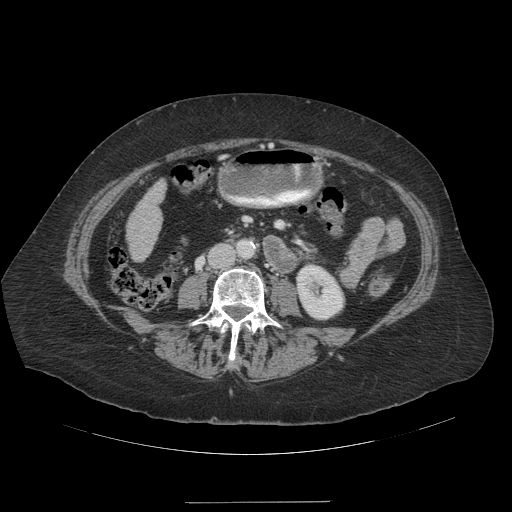
Contrast-enhanced abdominal CT (liver protocol), one axial slice. Slice 30 of 99 in the series (ordered by position). 140 kVp. Soft-tissue window (W 400 / L 40 HU). 2.5 mm slice thickness. 512 × 512 image matrix, field of view 440 × 440 mm. From the clinical record (not read from this slice): diagnosis: hepatocellular carcinoma (patient treated with transarterial chemoembolisation; whether this scan precedes or follows treatment is not stated here); TNM stage (as recorded): Stage-IVA; Child-Pugh class: A.
Annotated regions visible in this slice (semi-automatically segmented with operator editing):
- liver parenchyma outside the tumour (the mass and vessels are separate outlines, so this box may not span the whole liver): bounding box [x1, y1, x2, y2] px = [126, 180, 166, 260]